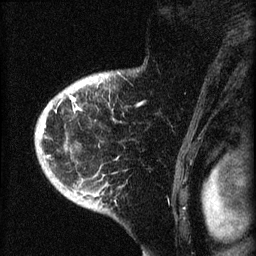
Breast MRI (dynamic contrast-enhanced), one sagittal slice; position 53 of 60 along the scan axis; dynamic contrast-enhanced series, image 2 of 4 at this slice position (ordered by acquisition); 1.5 T; TE 4.2 ms, TR 8.2 ms; 2 mm slice thickness; 256 × 256 image matrix, field of view 180 × 180 mm. Female patient, age 71 years.
Outlined on this slice (semi-automatic segmentation, software-assisted and operator-edited):
- analysis volume of interest (the breast-tissue region the enhancement analysis was run in; not a lesion): bounding box (x1, y1, x2, y2) in pixels: (35, 75, 128, 190)
- tumour enhancement mask (voxels above the 70 % enhancement threshold inside the analysis volume of interest): (41, 82, 114, 157)